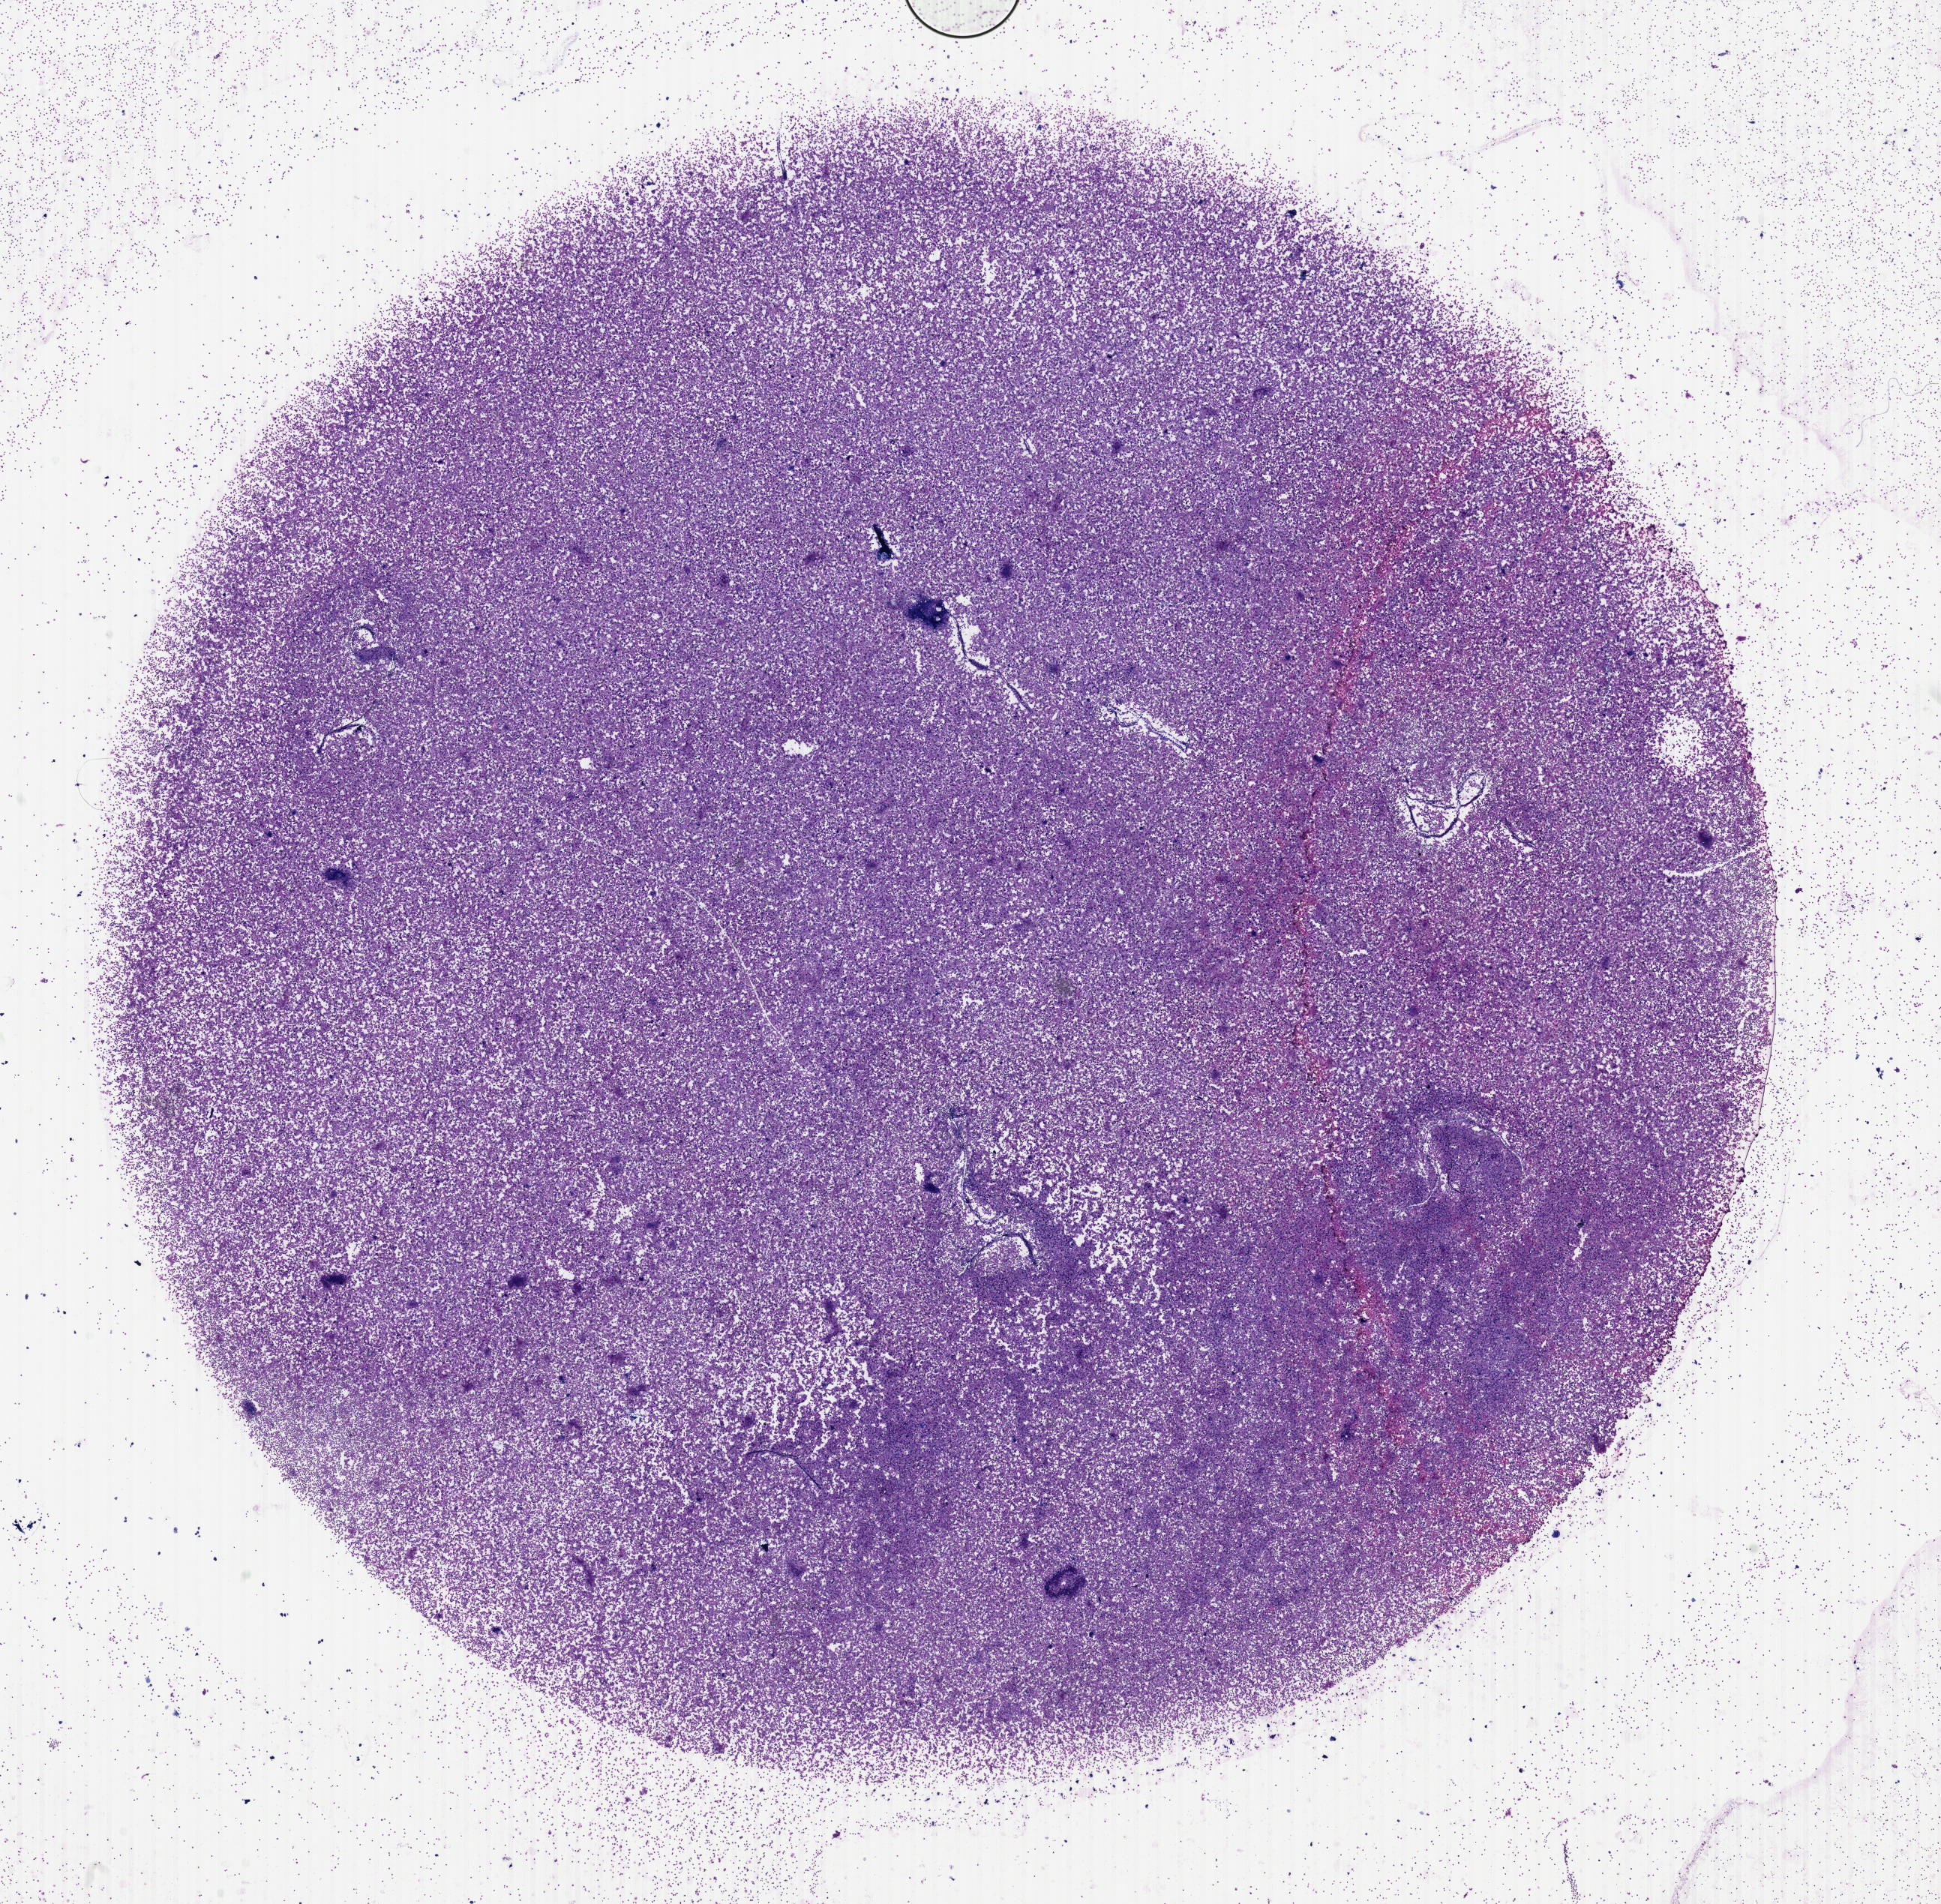
H&E whole-slide image — shown as a low-resolution overview of the whole scanned area (about 20.4 x 20.0 mm, from a 40x scan), bone marrow (leukaemic) sample. Male, 69 y/o. Blasts: 95%.
* WHO classification: AML with minimal differentiation
* FAB classification: M0
* diagnosis: Acute Myeloid Leukemia